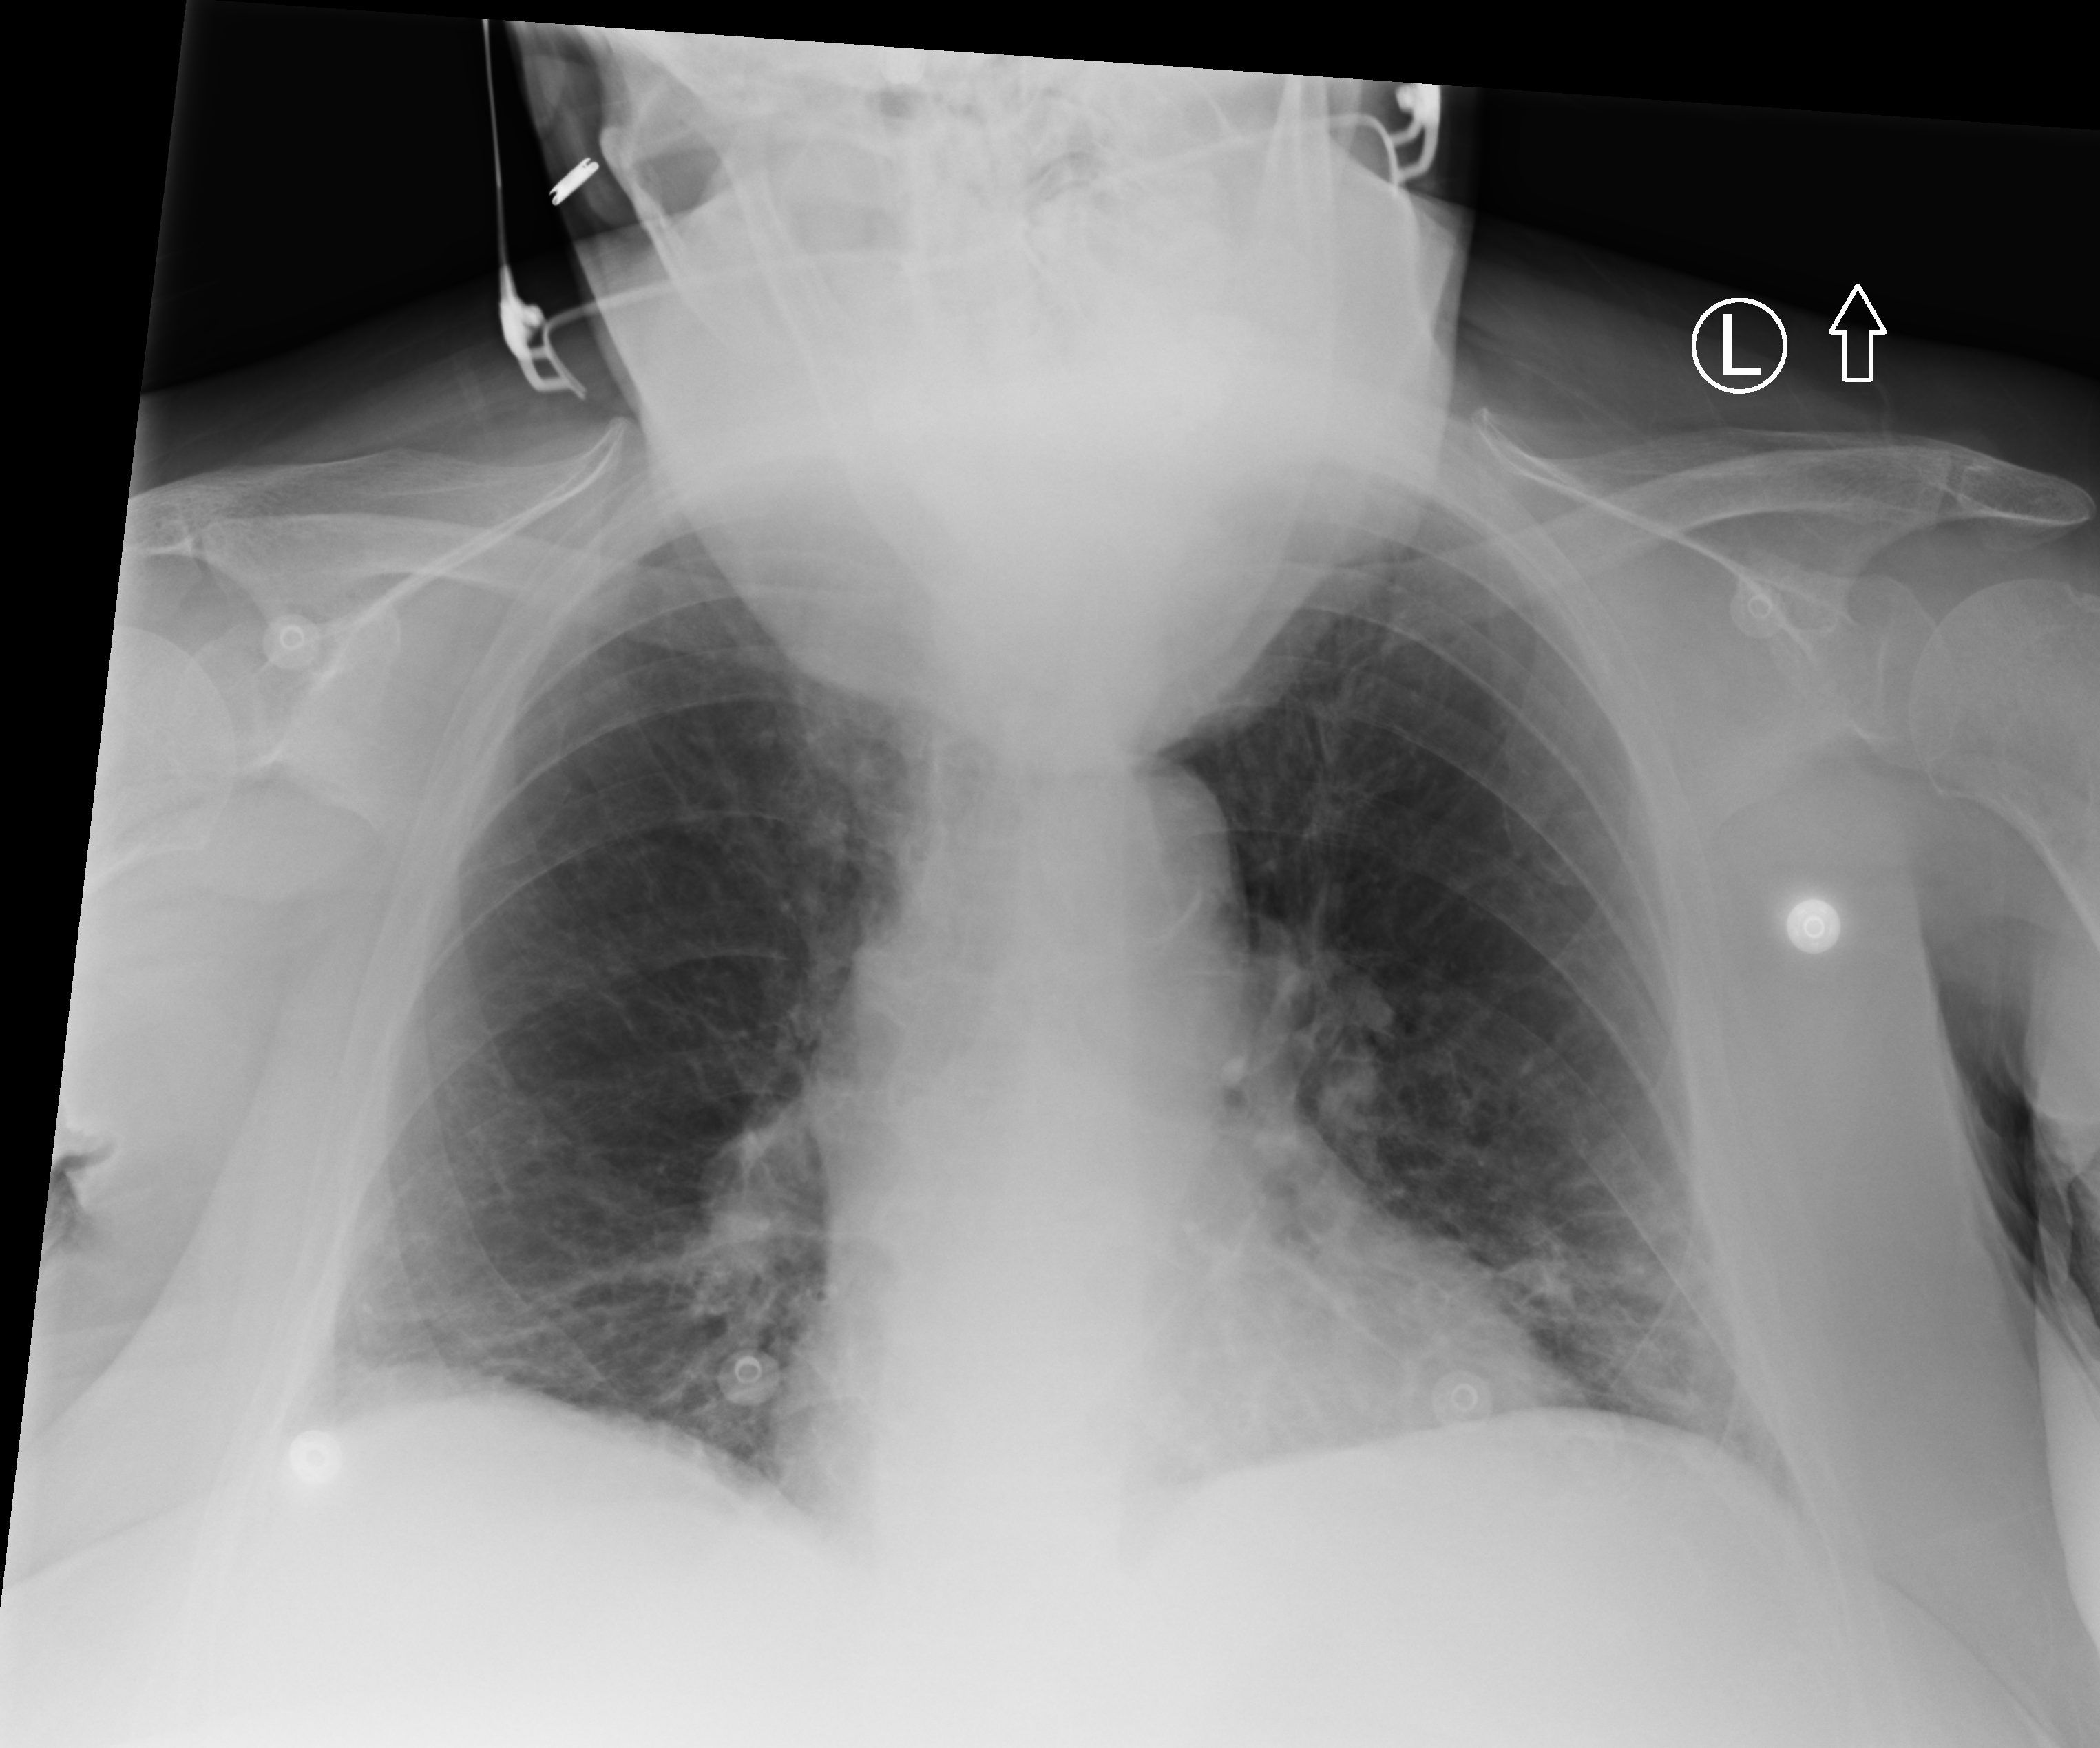
Portable chest radiograph. Female patient hospitalised with COVID-19, age 75–90 years.
Hospital-stay facts (about this admission, not read from this image; timing relative to this image not recorded): chronic kidney disease (admission record): yes; COPD (admission record): no.